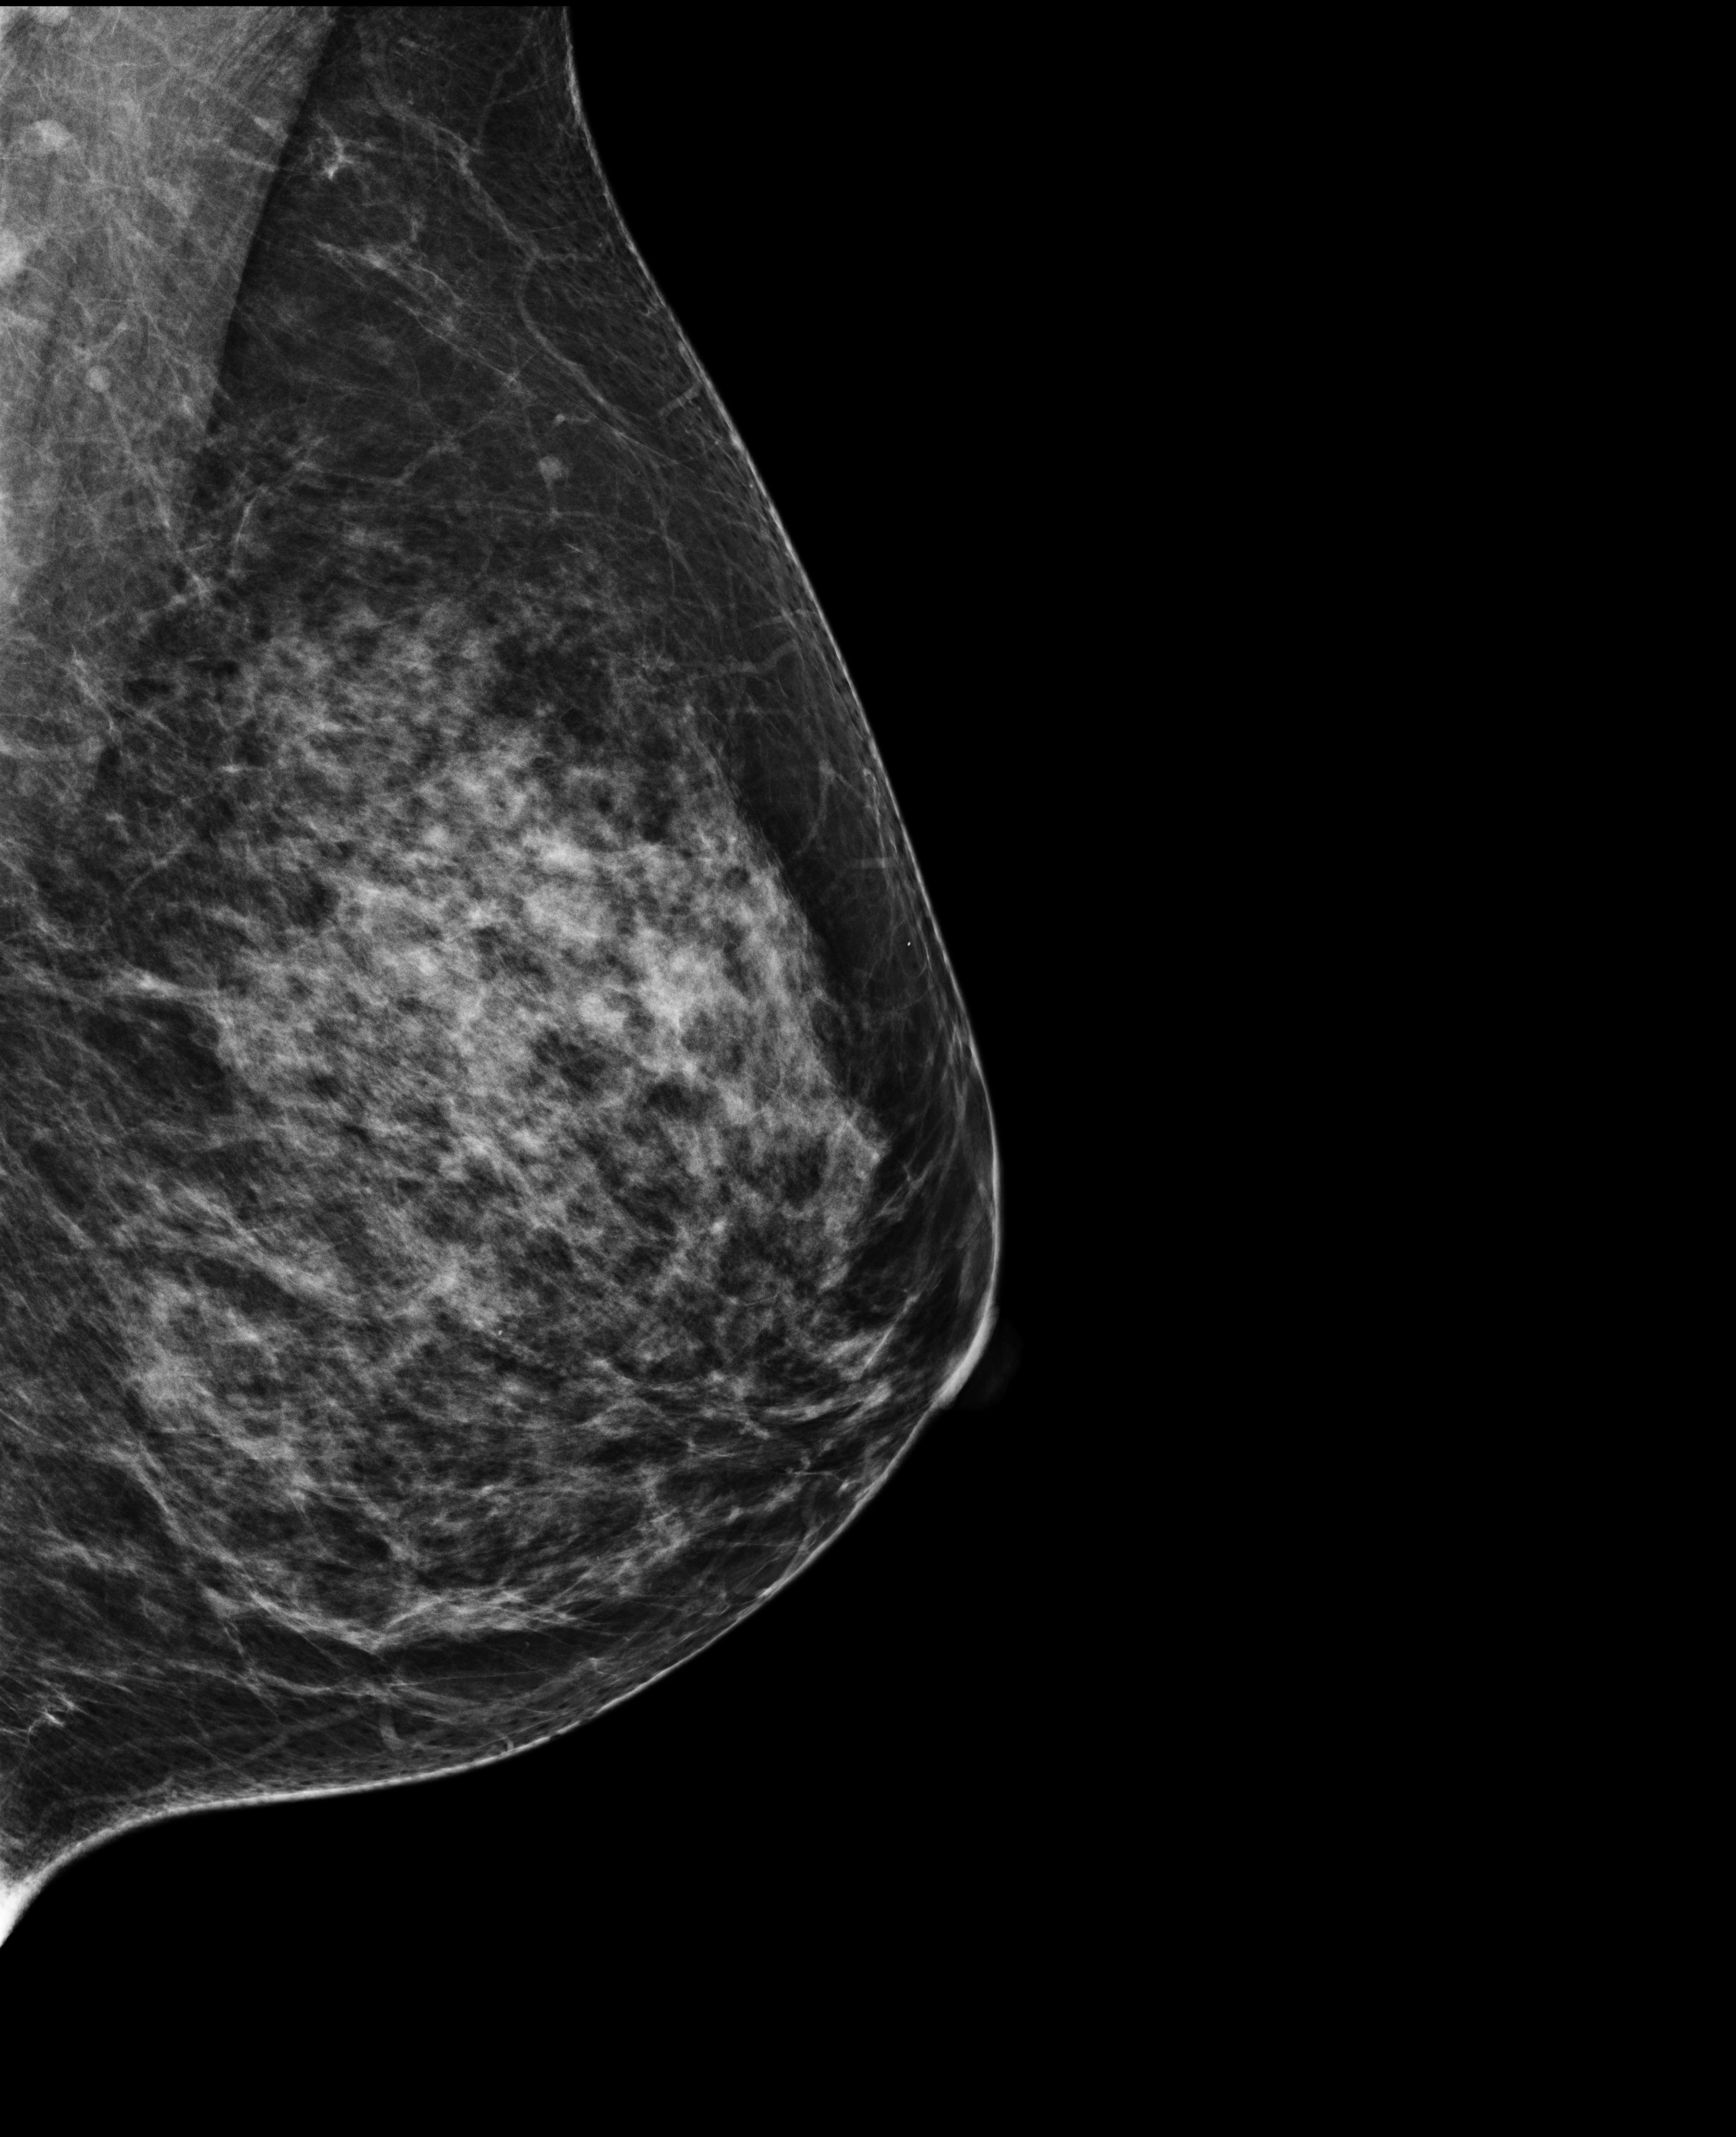
Screening examination; compressed breast thickness 73 mm. Patient: female, 47 years.
Image type: full-field digital mammogram. Breast: left. Projection: medio-lateral oblique projection.